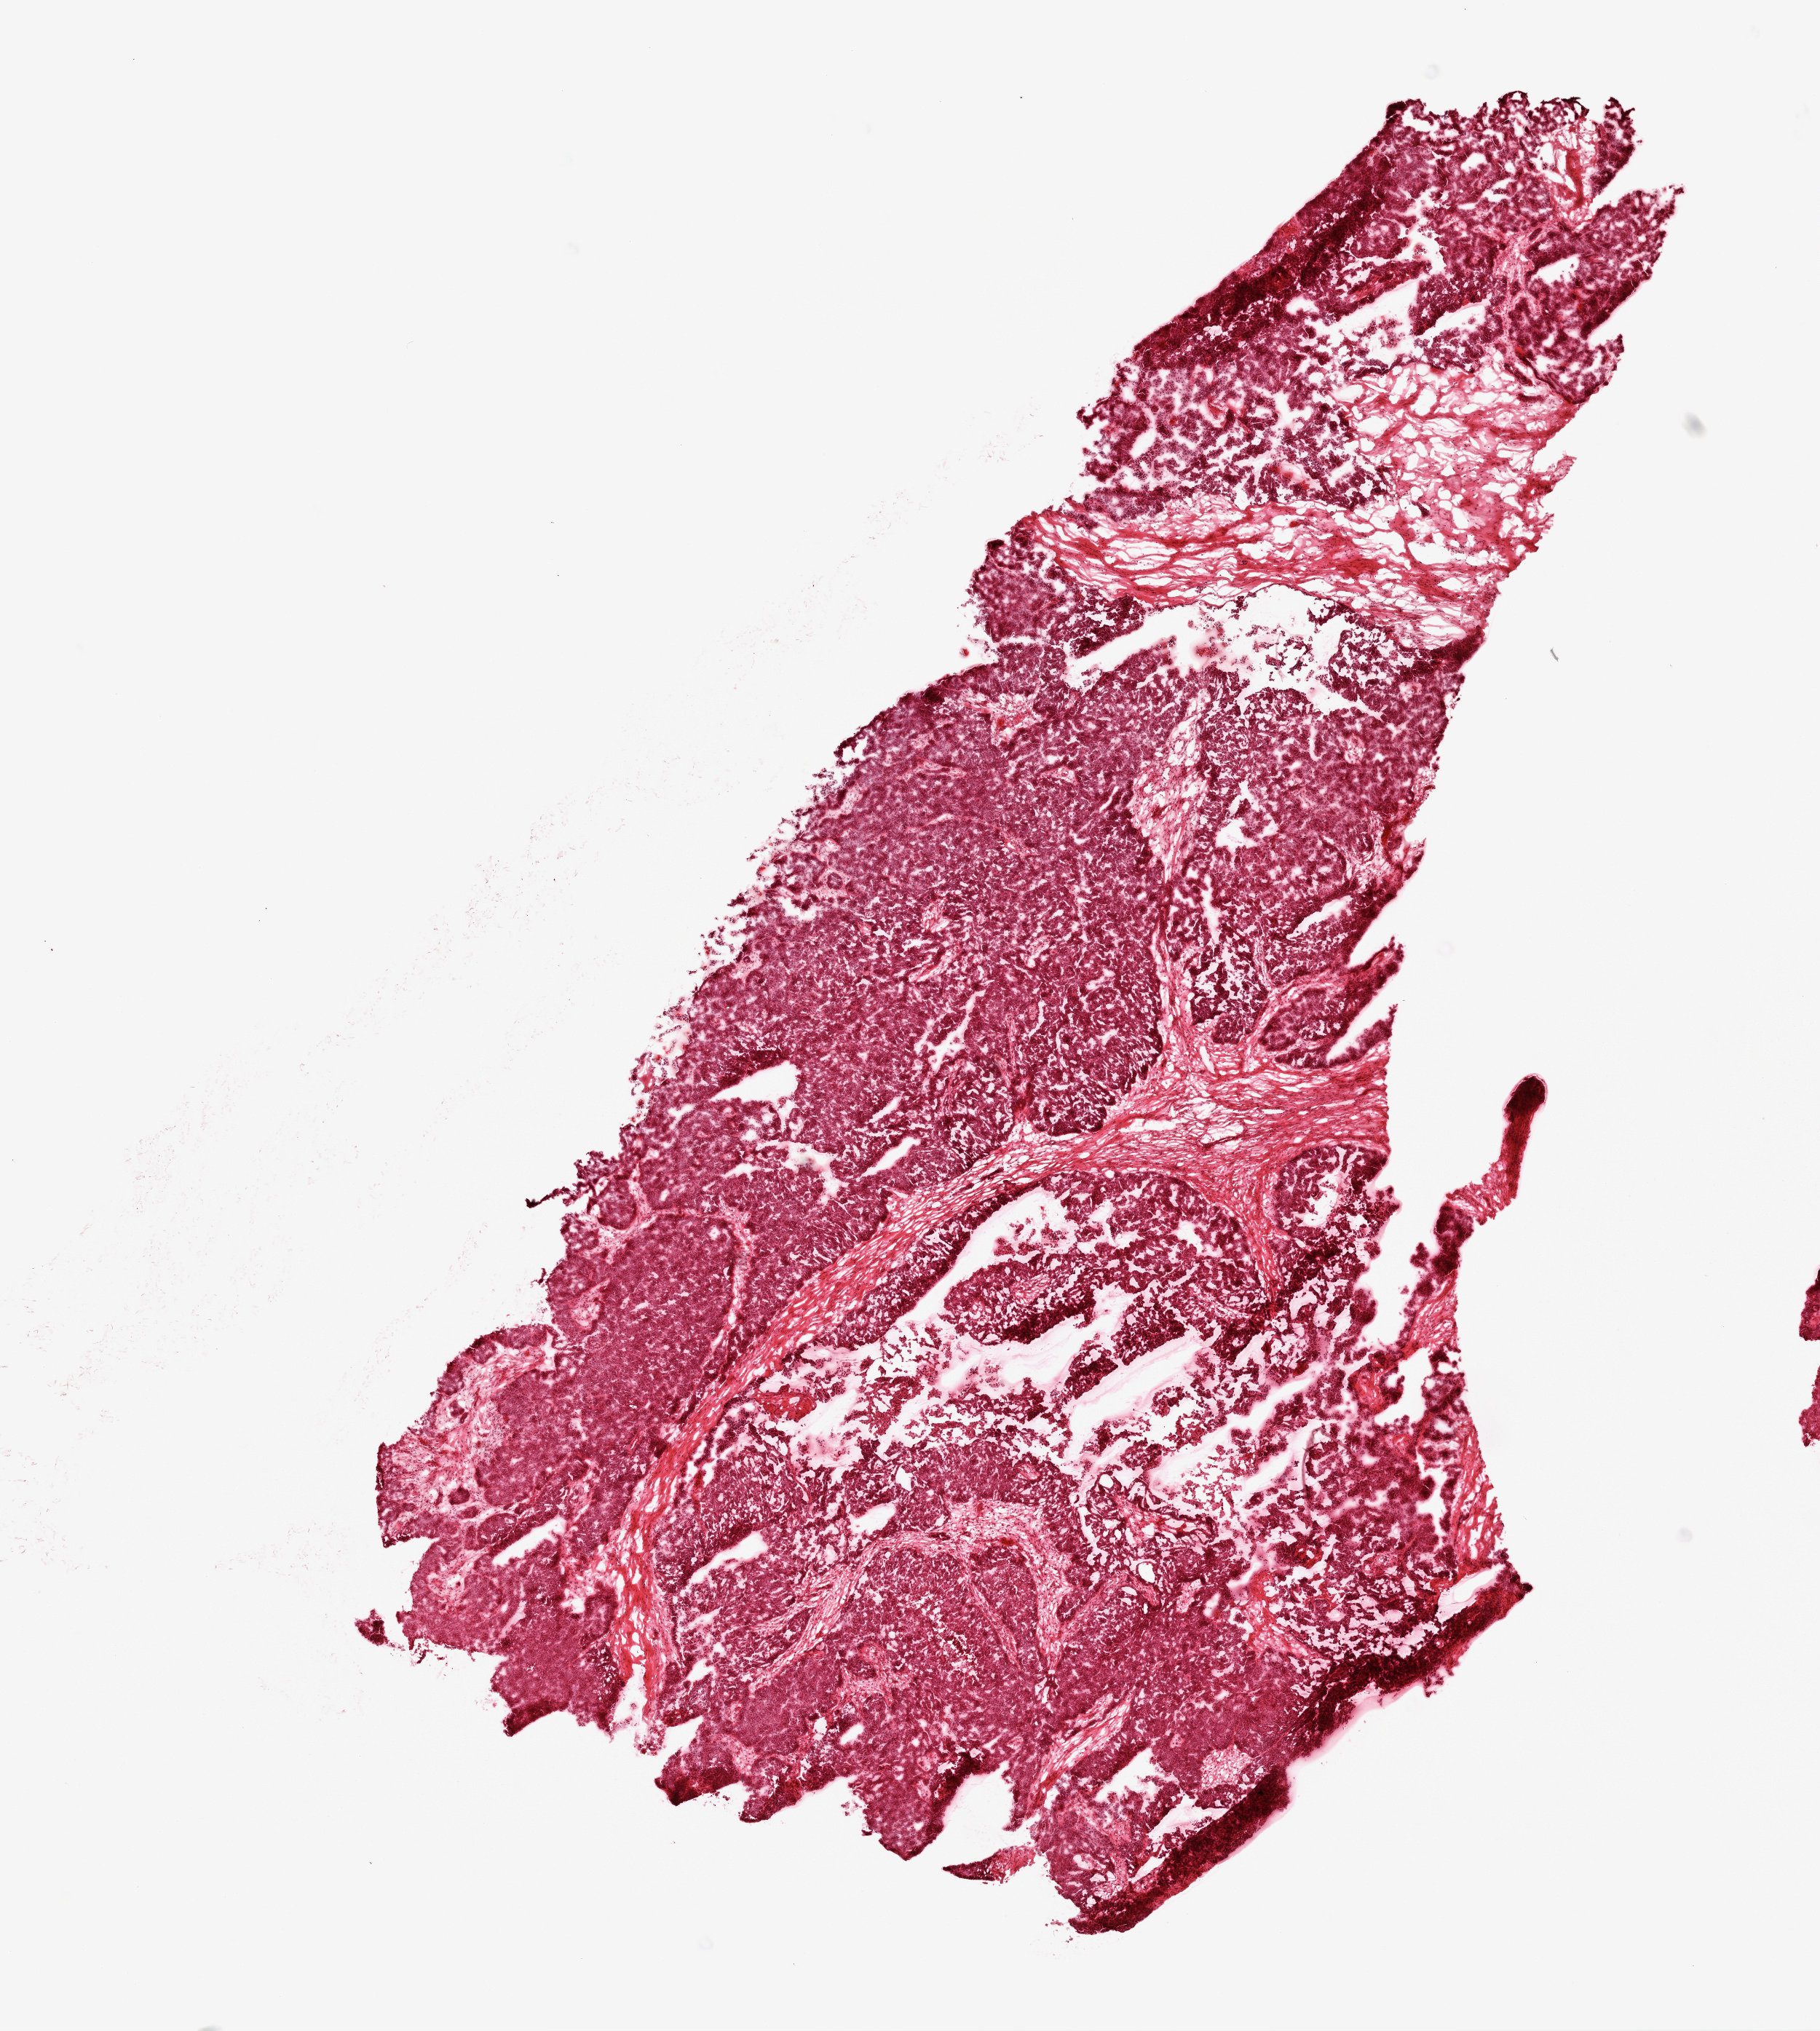
Whole-slide histology image, H&E — a low-resolution overview of the entire scanned area, about 10.0 x 11.2 mm; frozen section from the top of the tissue portion; ovary, primary tumour sample. Female, age 50 years at initial diagnosis. Histologic grade: G3 (poorly differentiated). Pathologist review of this section (percent, as recorded): tumour cells 80%, tumour nuclei 95%, normal cells 0%, stromal cells 20%, necrosis 0%.
FIGO stage: IIIC. Diagnosis: Serous cystadenocarcinoma, NOS. Laterality: bilateral.